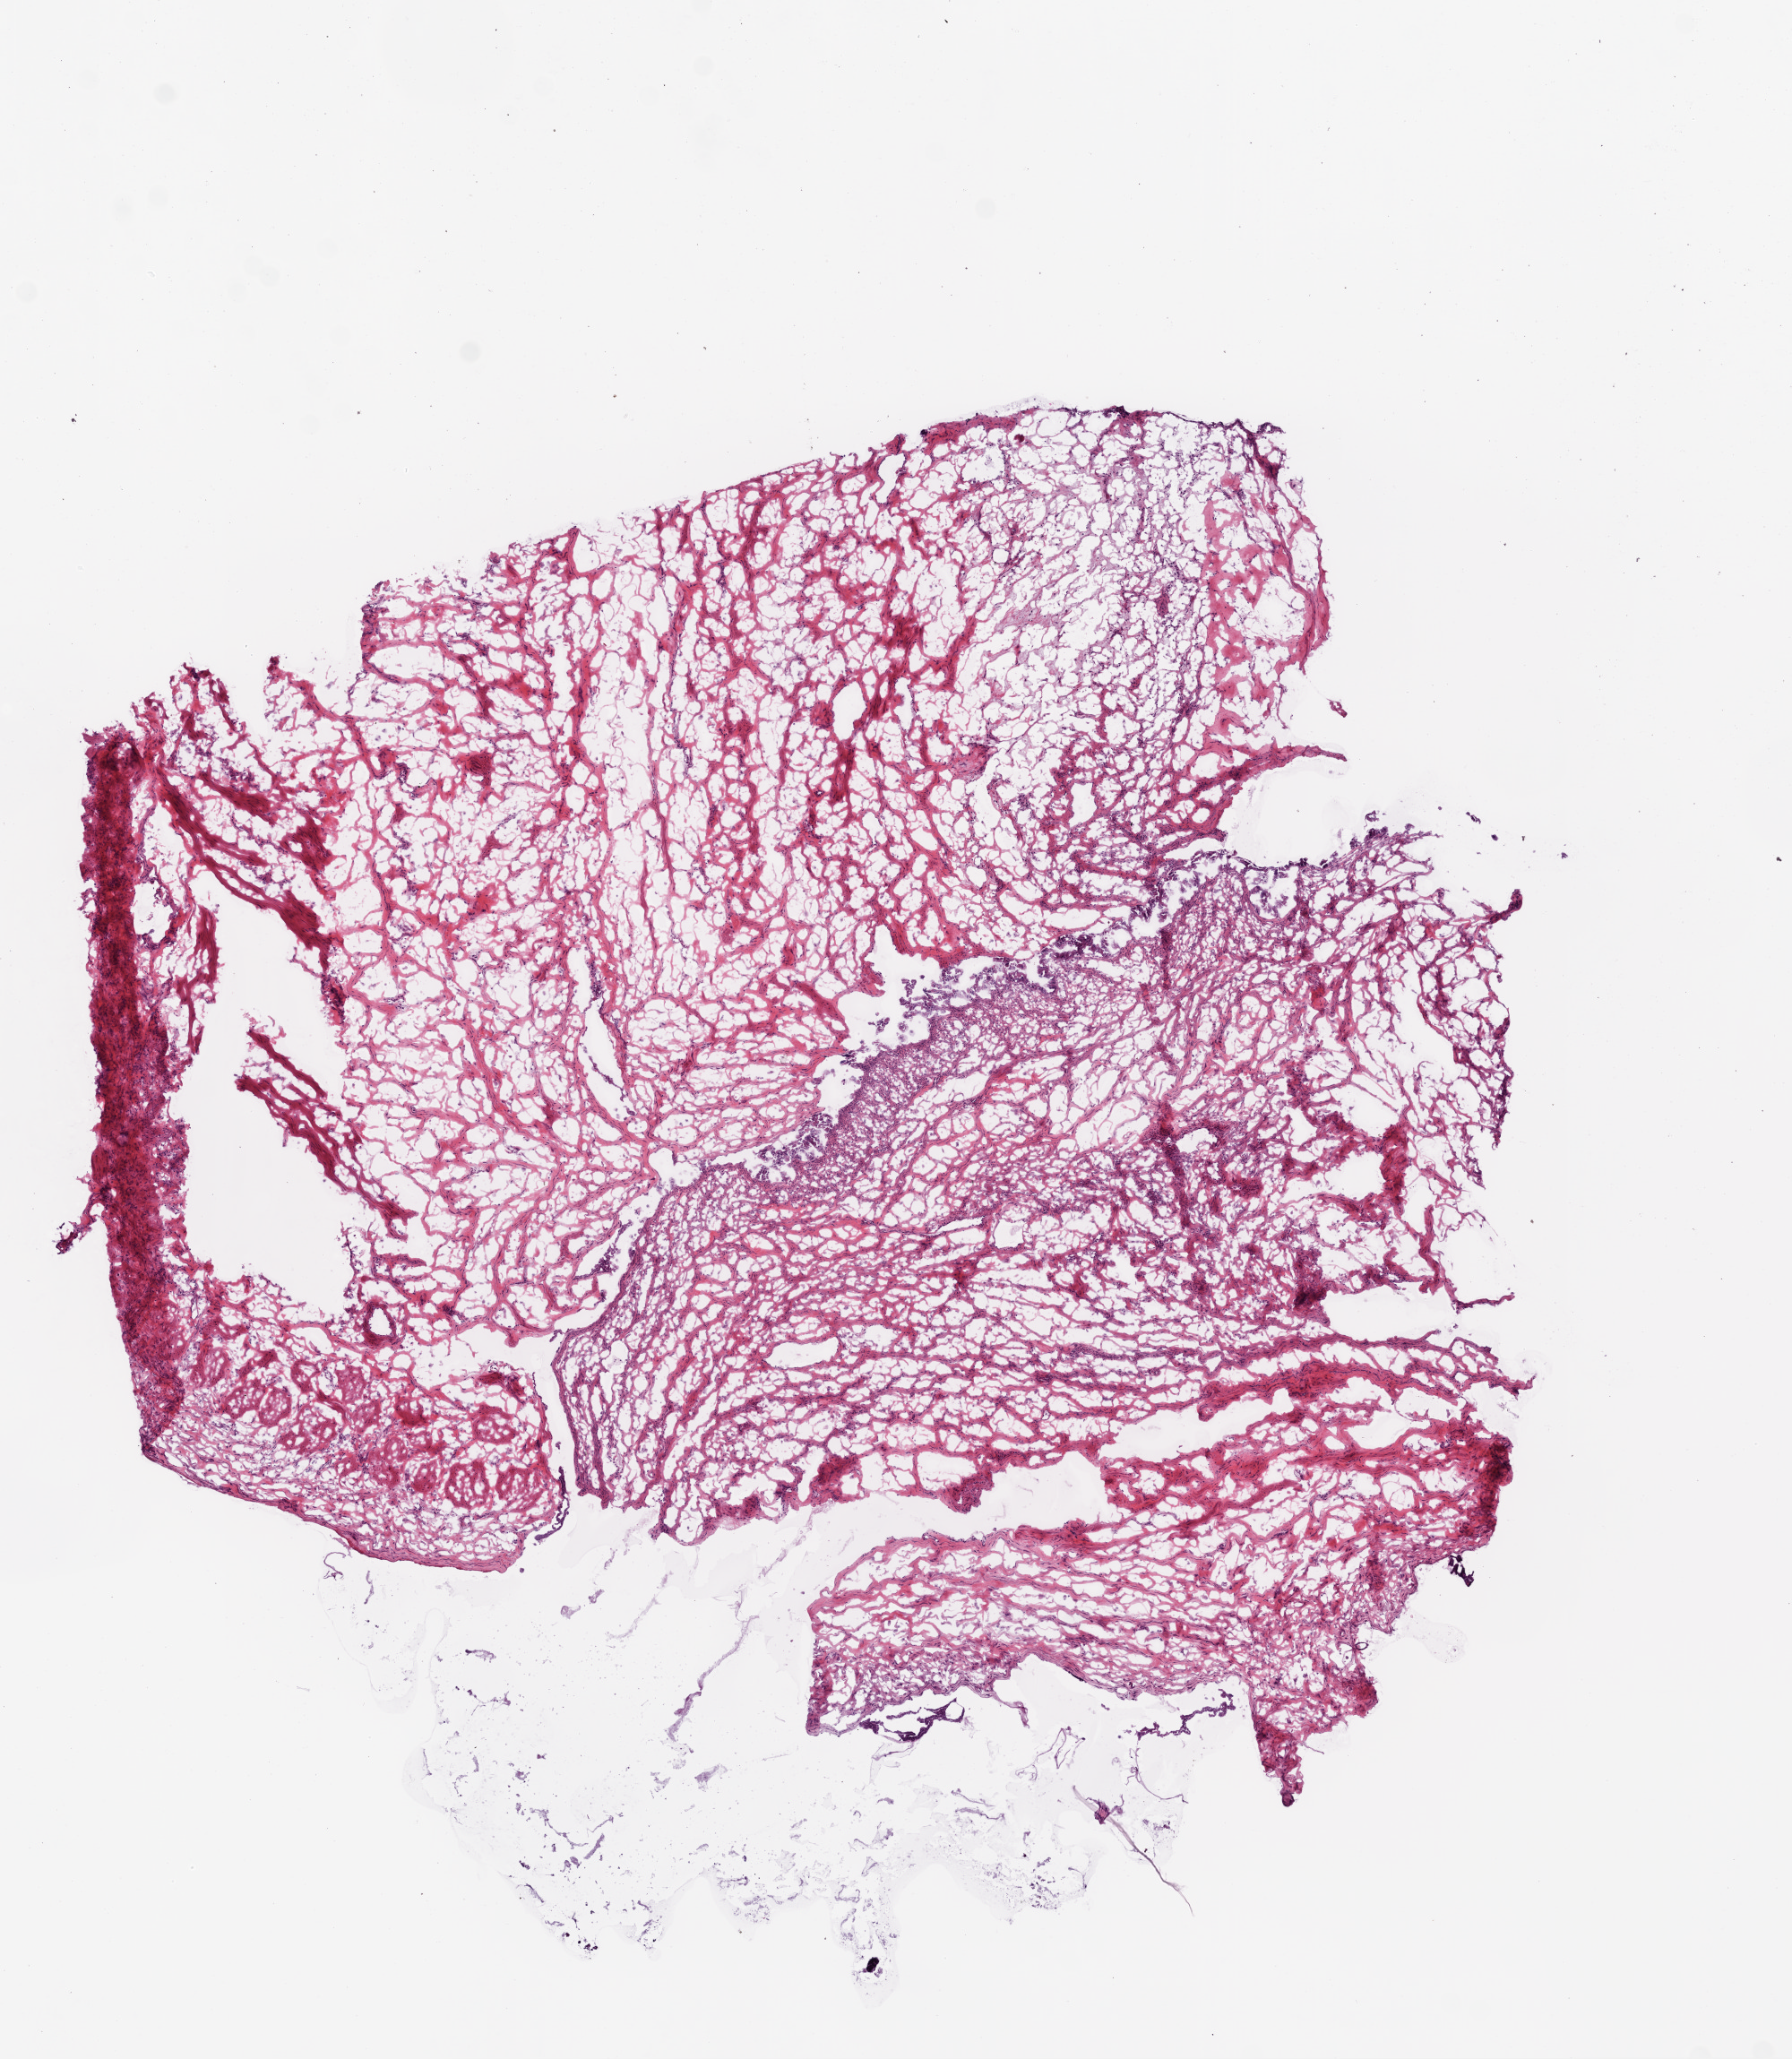
H&E whole-slide image, low-resolution overview of the scanned area, about 8.0 x 9.2 mm (acquisition: 20x scan); frozen section; solid tissue normal (non-tumour tissue) sample from the ovary. Female patient; age at initial diagnosis 56 years.
- this section: solid tissue normal (non-tumour) sample from the same patient
- patient diagnosis: Serous cystadenocarcinoma, NOS